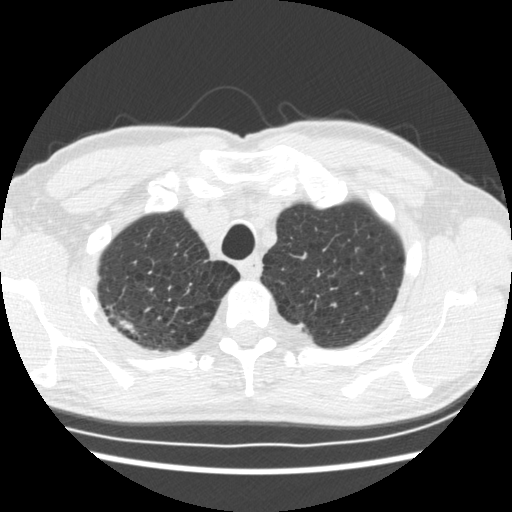
Low-dose screening chest CT, one axial slice. Position 155 of 183 along the scan axis. 120 kVp. Lung window (W 1500 / L -600 HU). 2.5 mm slice thickness. 512 × 512 image matrix, field of view 339 × 339 mm.
Annotated regions visible in this slice (outlined manually by an expert reader):
- lesion 1 (tumor, upper lobe of right lung): box from (x=118, y=316) to (x=139, y=337) px